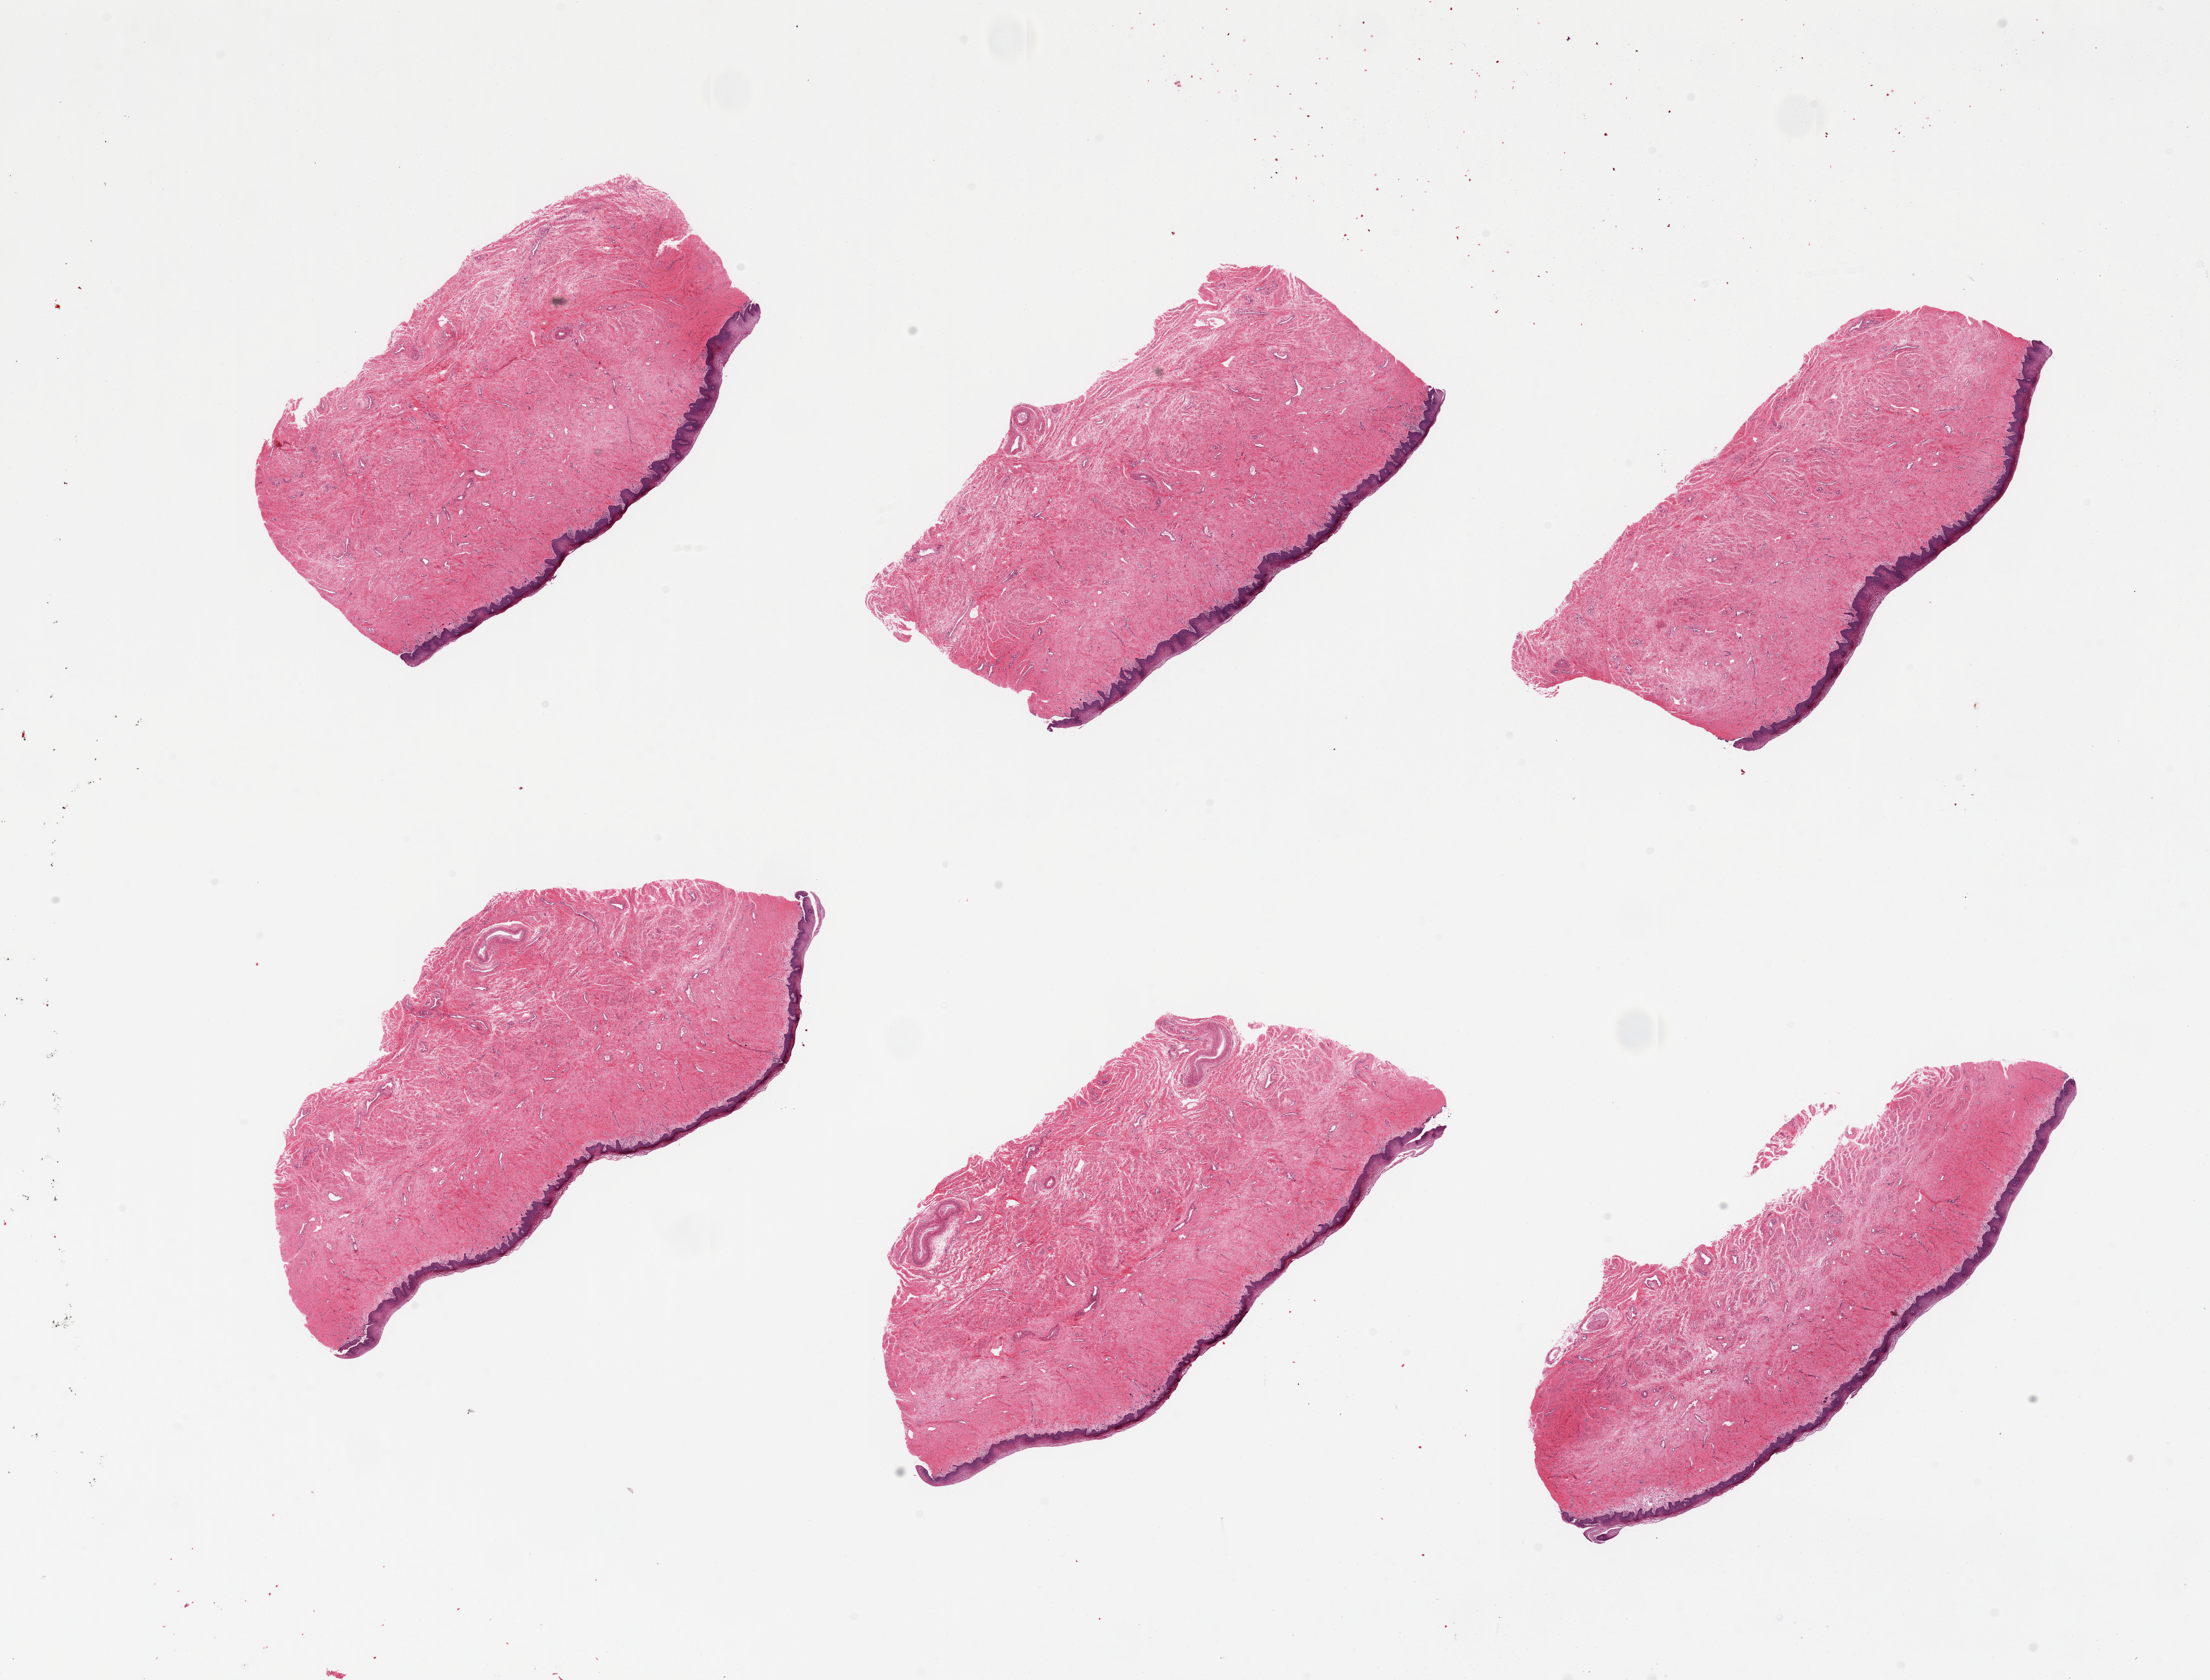
Whole-slide image, haematoxylin and eosin stain — a low-resolution overview of the entire scanned area, about 27.6 x 21.0 mm (slide scanned at 20x); PAXgene-fixed, paraffin-embedded tissue; section of vagina (target tissue); donor tissue sample. Female donor.
Review note (as recorded): 6 pieces.